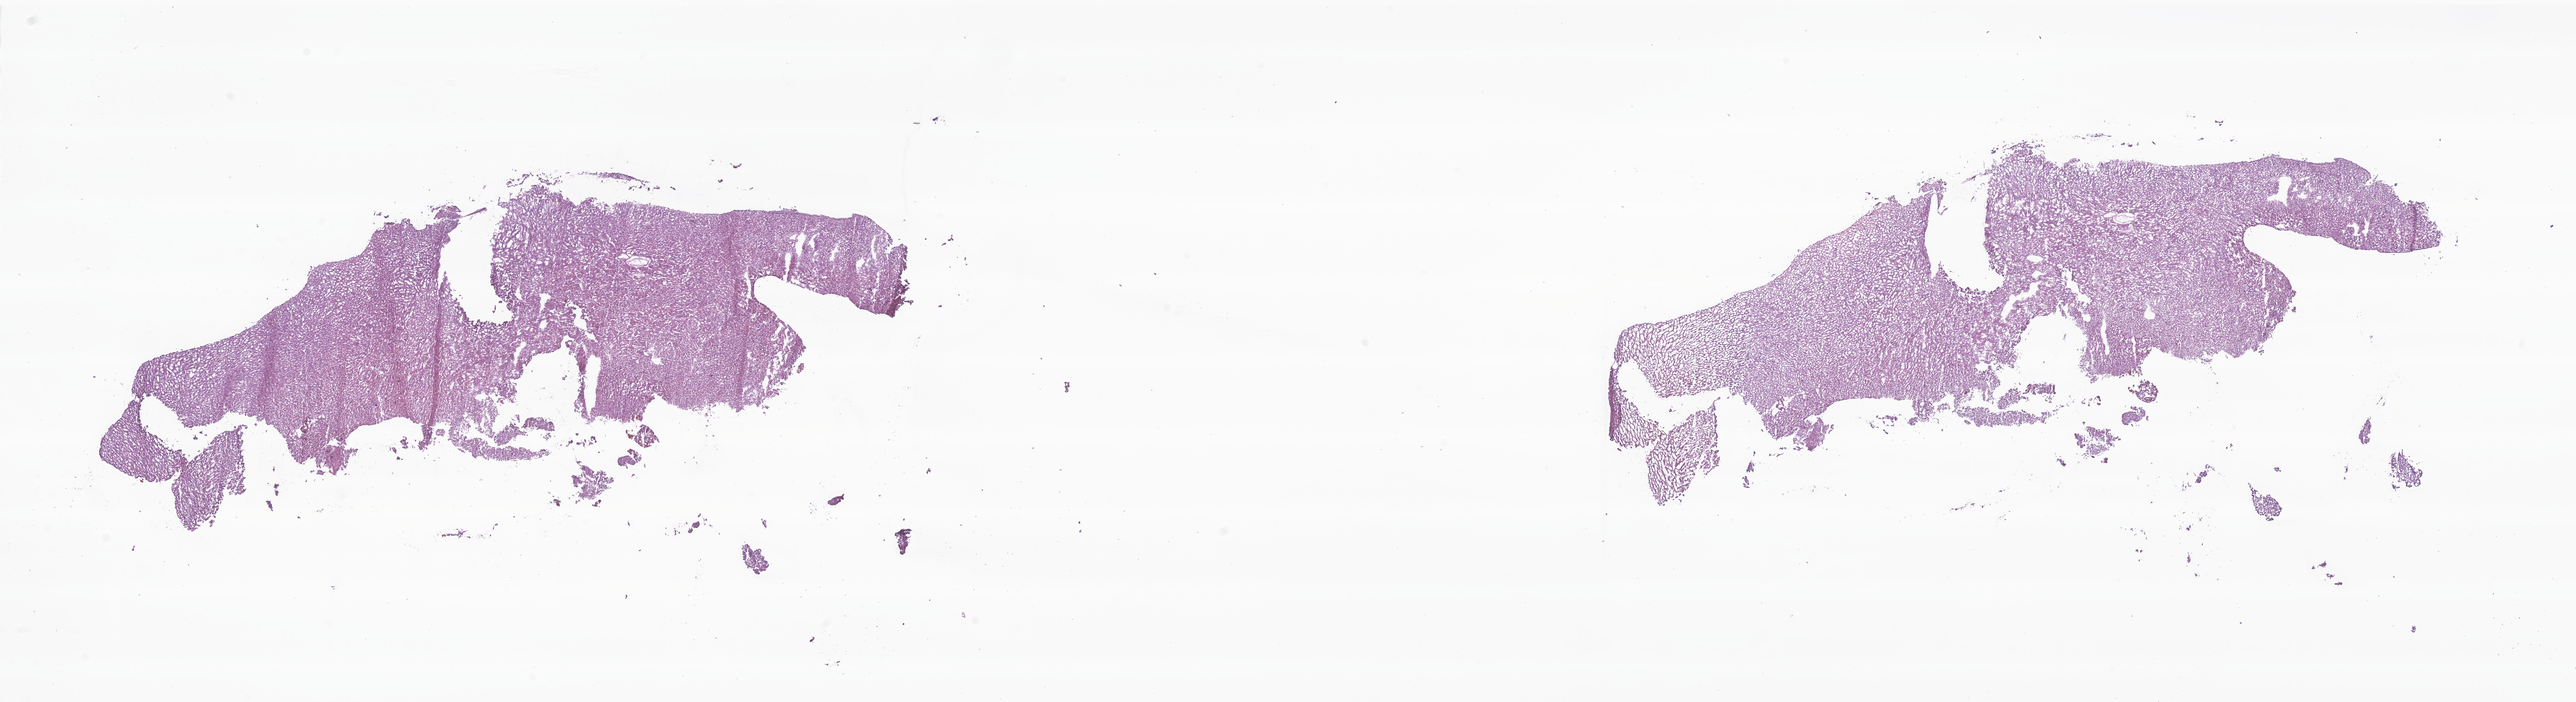
Whole-slide image, haematoxylin and eosin stain of tumor tissue from the brain — shown as a low-resolution overview of the whole scanned area (about 35.9 x 9.8 mm); cryosection (OCT / tissue freezing medium). Patient: male, age 321 days.
- diagnosis: Ependymoma, NOS